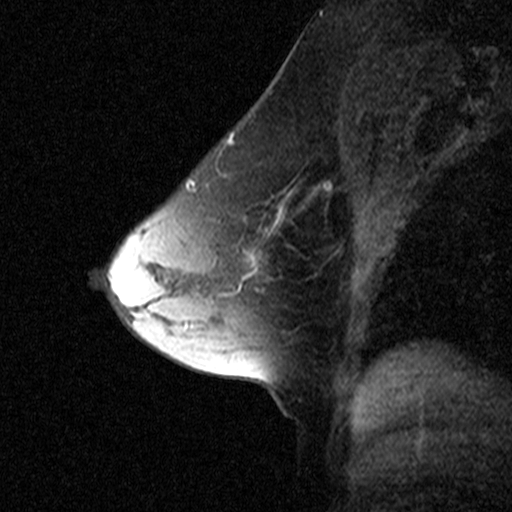
Breast MRI (dynamic contrast-enhanced), one sagittal slice; slice 28 of 44 in the series (ordered by position); dynamic contrast-enhanced study with each time point stored as its own series, time point 2 of 3 at this slice position (early post-contrast, ordered by acquisition time); 1.5 T; TE 4.5 ms, TR 11 ms; 3 mm slice thickness; 512 × 512 image matrix, field of view 200 × 200 mm. Patient: female, 53 years. From the clinical record (not read from this slice): setting: breast cancer imaged before/during neoadjuvant chemotherapy; receptor status: HR-positive, HER2-negative.
Annotated regions visible in this slice (semi-automatic segmentation, software-assisted and operator-edited):
- analysis volume of interest (the breast-tissue region the enhancement analysis was run in; not a lesion): bounding box <170,150,277,273> (left, top, right, bottom; pixels)
- tumour enhancement mask (voxels above the 90 % enhancement threshold inside the analysis volume of interest): <189,181,191,183>